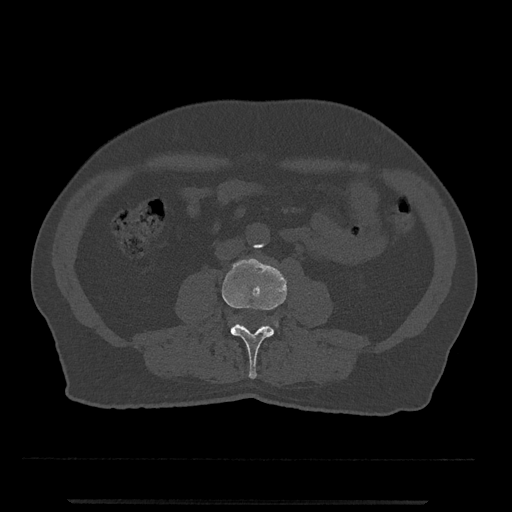
CT including the spine, one axial slice. Position 187 of 797 along the scan axis. Reconstruction kernel Br40s/3. Bone window (W 1800 / L 400 HU). 0.5 mm slice thickness. 512 × 512 image matrix, field of view 419 × 419 mm. Patient: male, 63 years. From the clinical record (not read from this slice): primary cancer: prostate.
Structures marked on this image (semi-automatically segmented with operator editing):
- L3 vertebra: bounding box (x1, y1, x2, y2) in pixels: (222, 258, 287, 379)
- L4 vertebra: (228, 319, 279, 328)